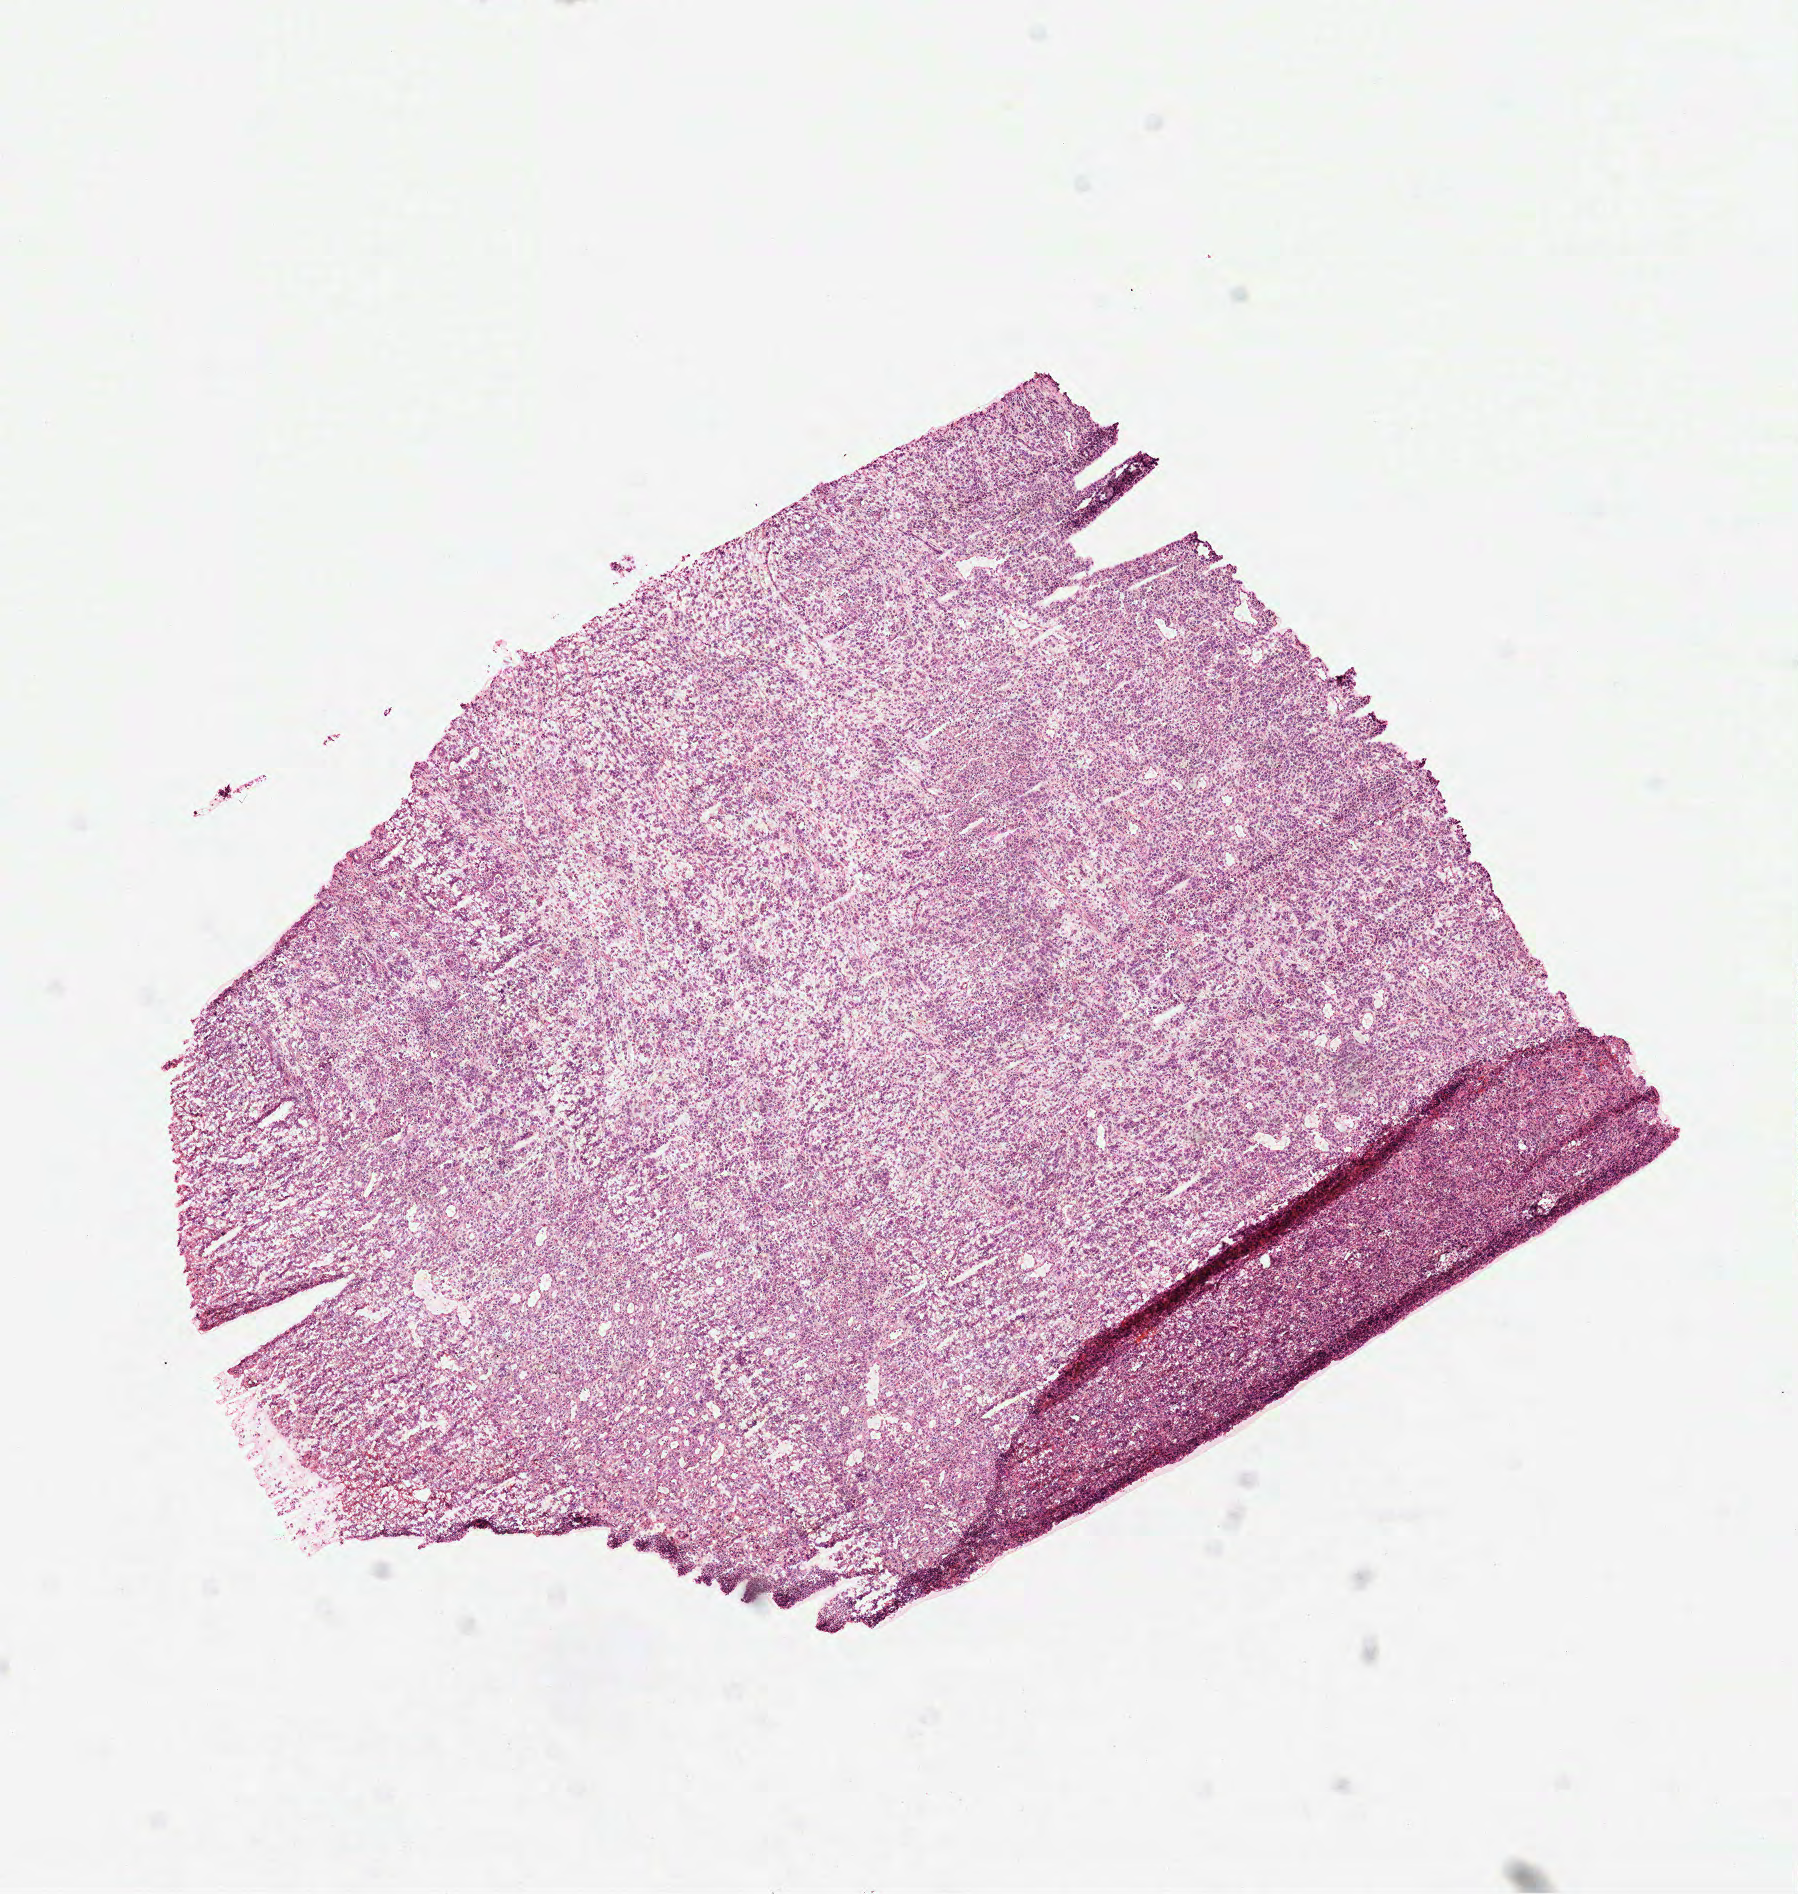
Digitized H&E-stained tissue section (whole slide), whole scanned area (about 7.3 x 7.6 mm) shown as a low-resolution overview; frozen section from the top of the tissue portion; sample: primary tumour, stomach. Male, age 53 years at initial diagnosis. Histologic grade: G3 (poorly differentiated). Pathologist review of this section (percent, as recorded): tumour cells 90%, tumour nuclei 80%, normal cells 0%, stromal cells 10%, necrosis 0%.
* TNM: T2 N1 M0
* AJCC pathologic stage: II (6th edition)
* histologic diagnosis: Carcinoma, diffuse type (gastric antrum)